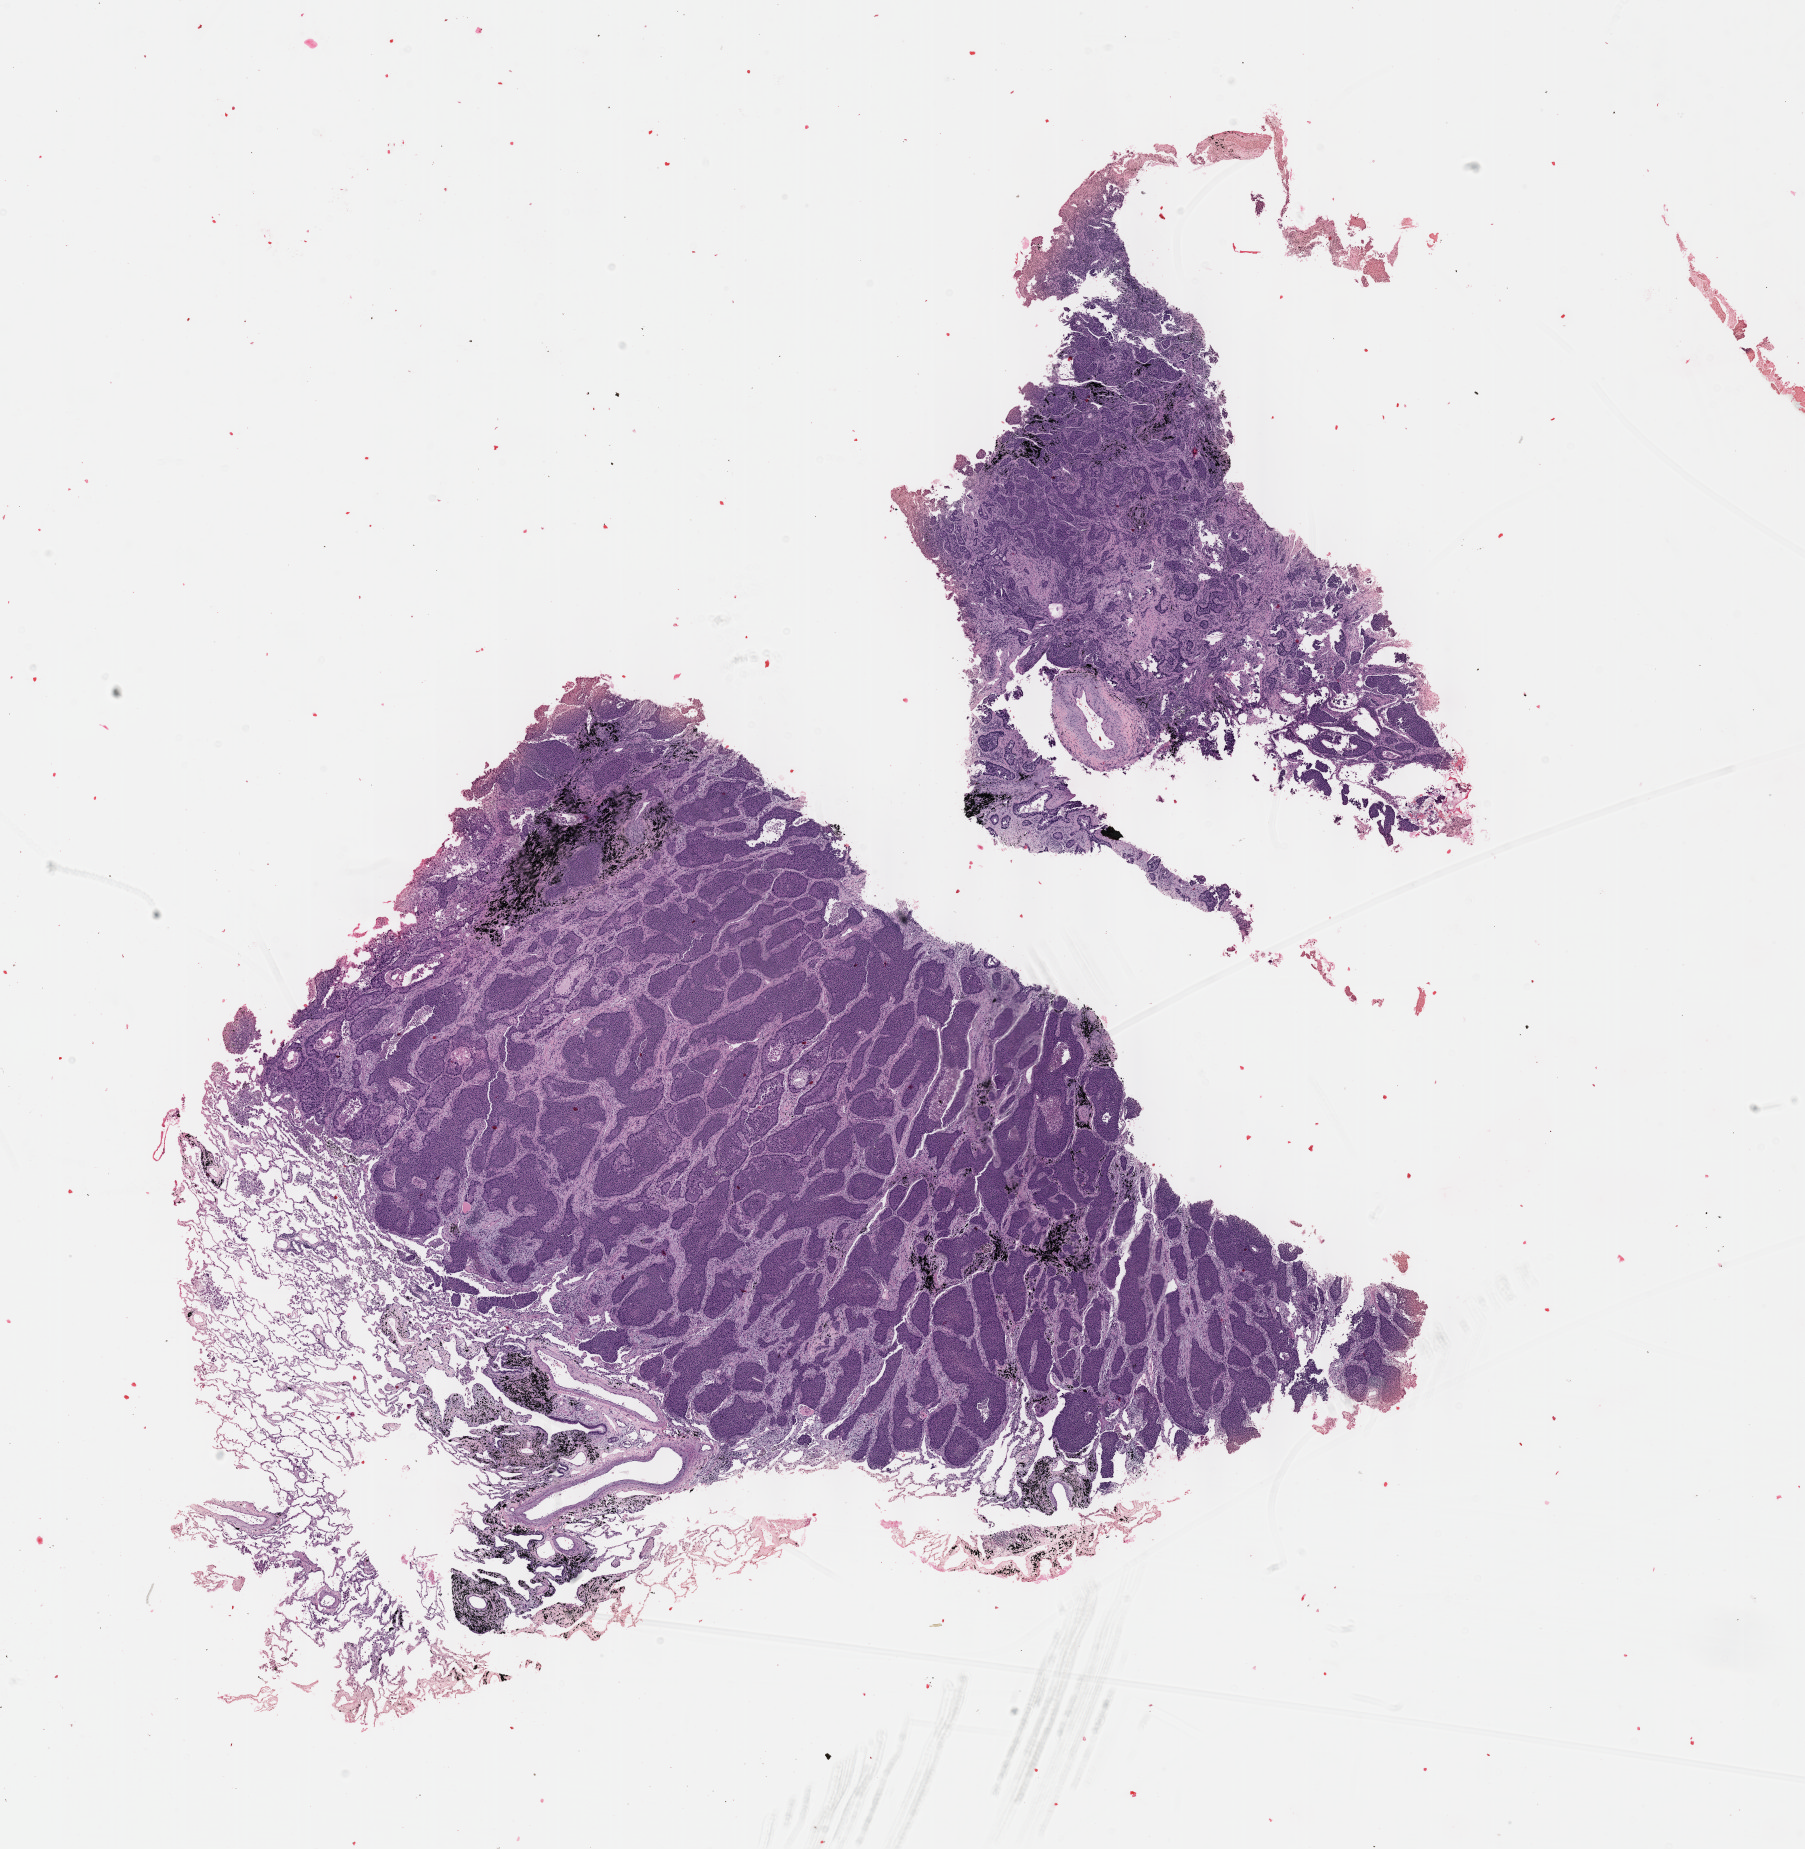
Whole-slide histology image, H&E-stained, low-resolution overview of the scanned area, about 14.6 x 14.9 mm (slide scanned at 40x), formalin-fixed paraffin-embedded (FFPE) diagnostic section, sample: primary tumour, lung. Male patient; age at initial diagnosis 68 years.
Diagnosis: Adenocarcinoma, NOS (upper lobe, lung).